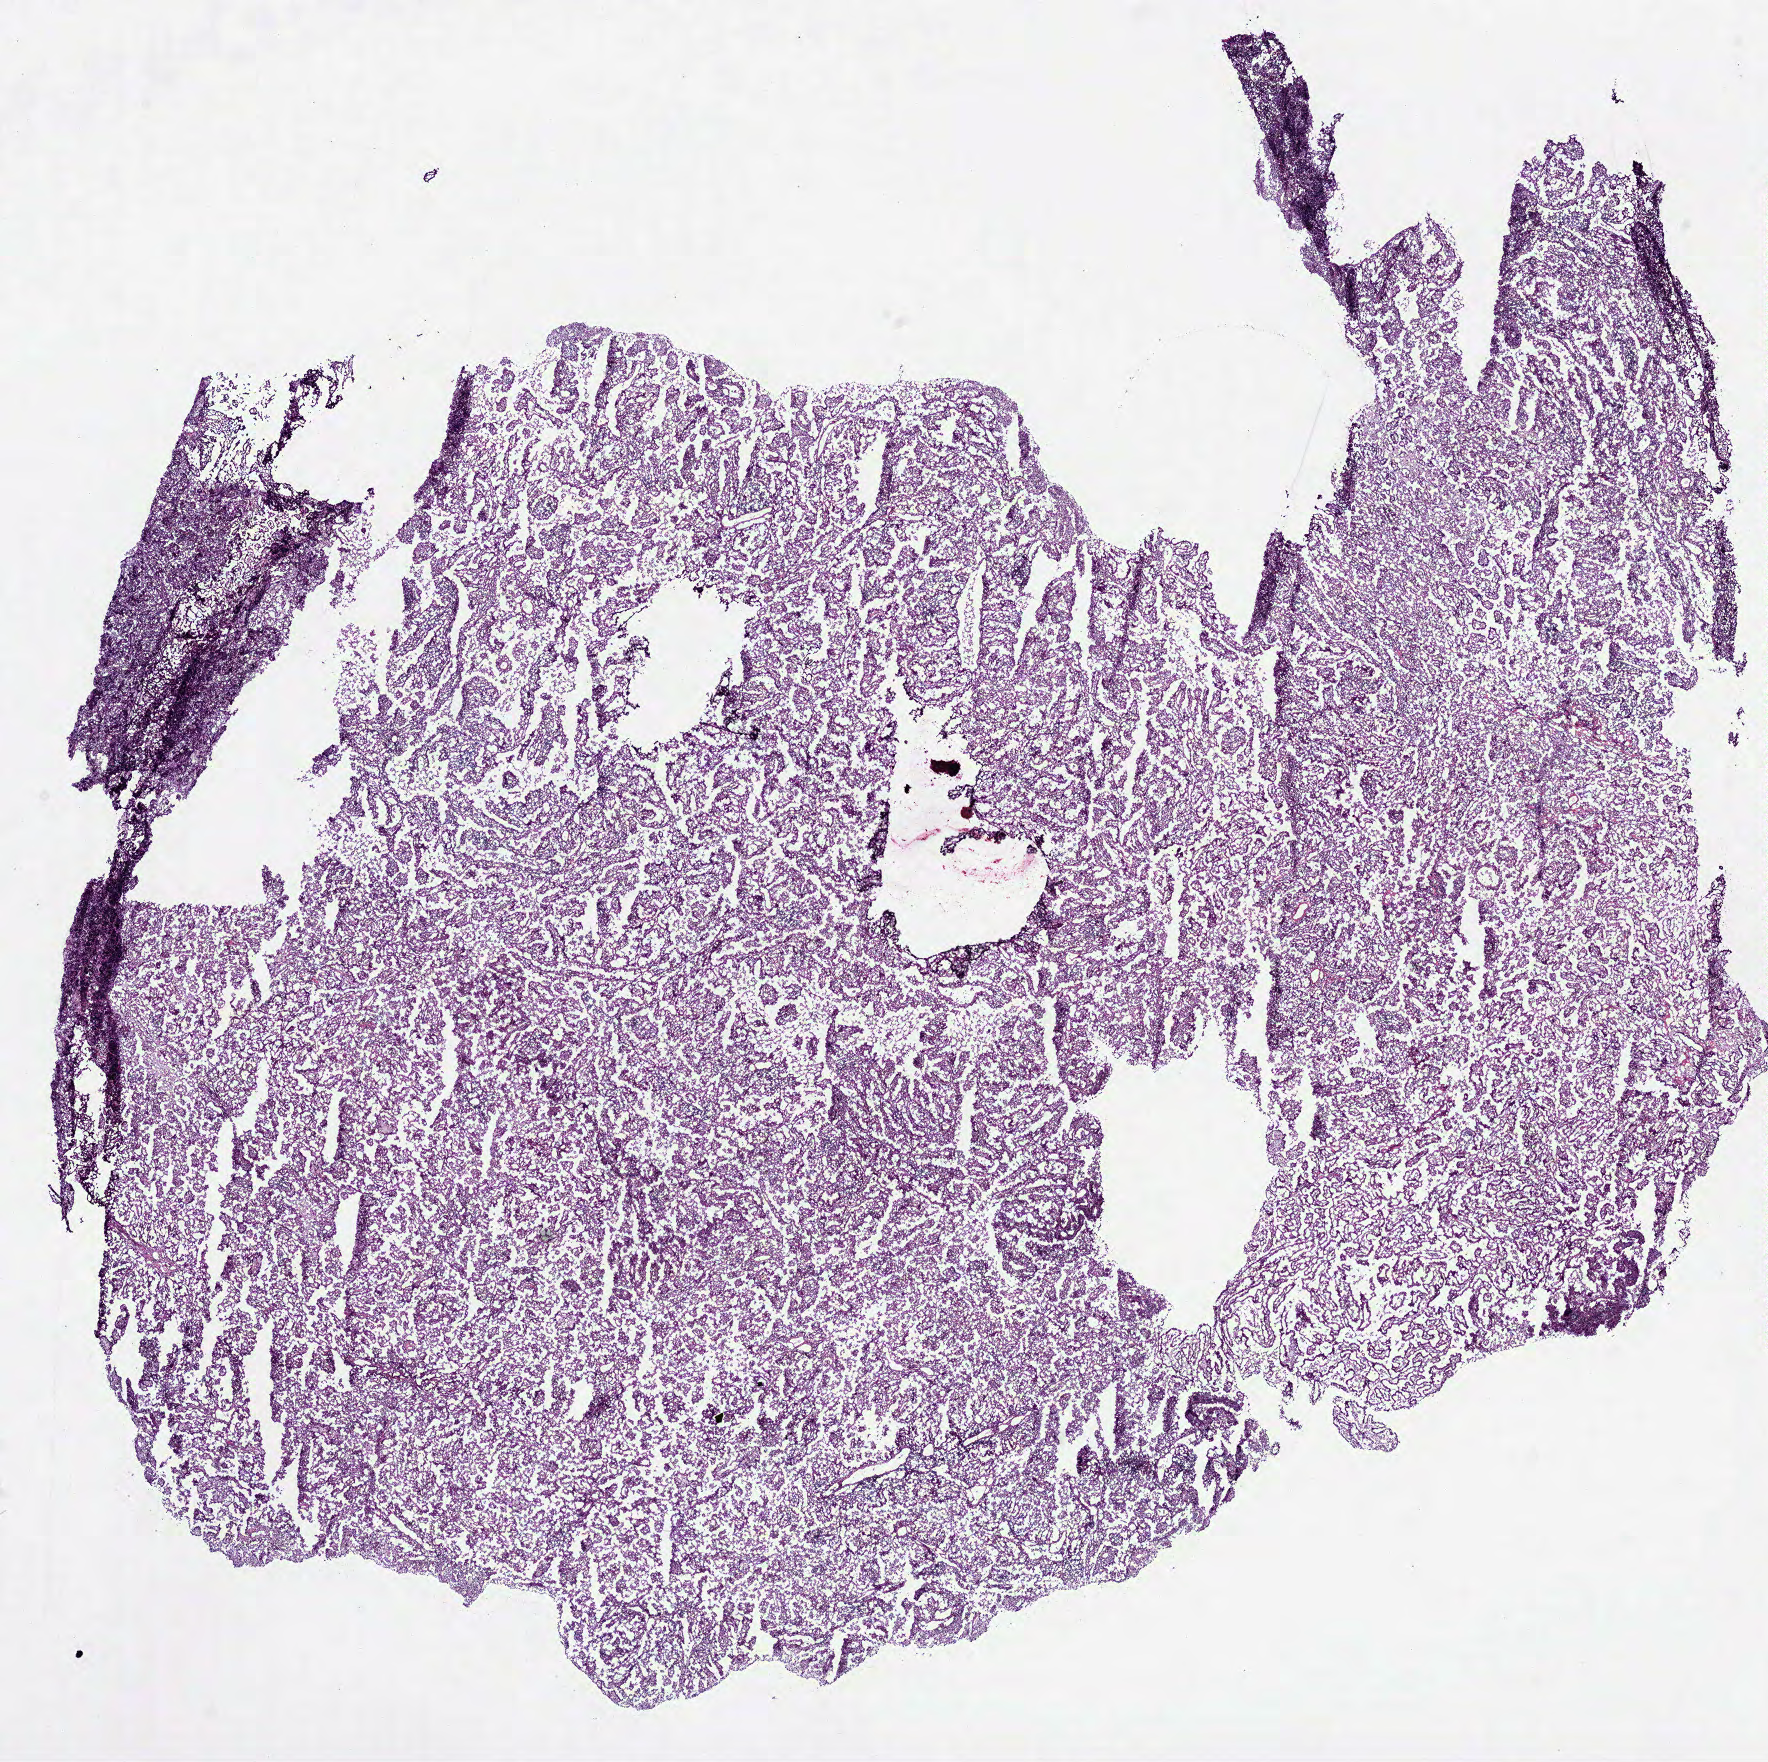
Digitized H&E-stained tissue section (whole slide), low-resolution overview of the scanned area, about 14.3 x 14.2 mm (from a 40x scan); frozen section from the bottom of the tissue portion; kidney, primary tumour sample. Female patient; age at initial diagnosis 74 years. Slide review estimates, as recorded: tumour cells 92%, tumour nuclei 85%, normal cells 0%, stromal cells 5%, necrosis 3%.
* AJCC pathologic stage: I
* pathologic diagnosis: Papillary adenocarcinoma, NOS